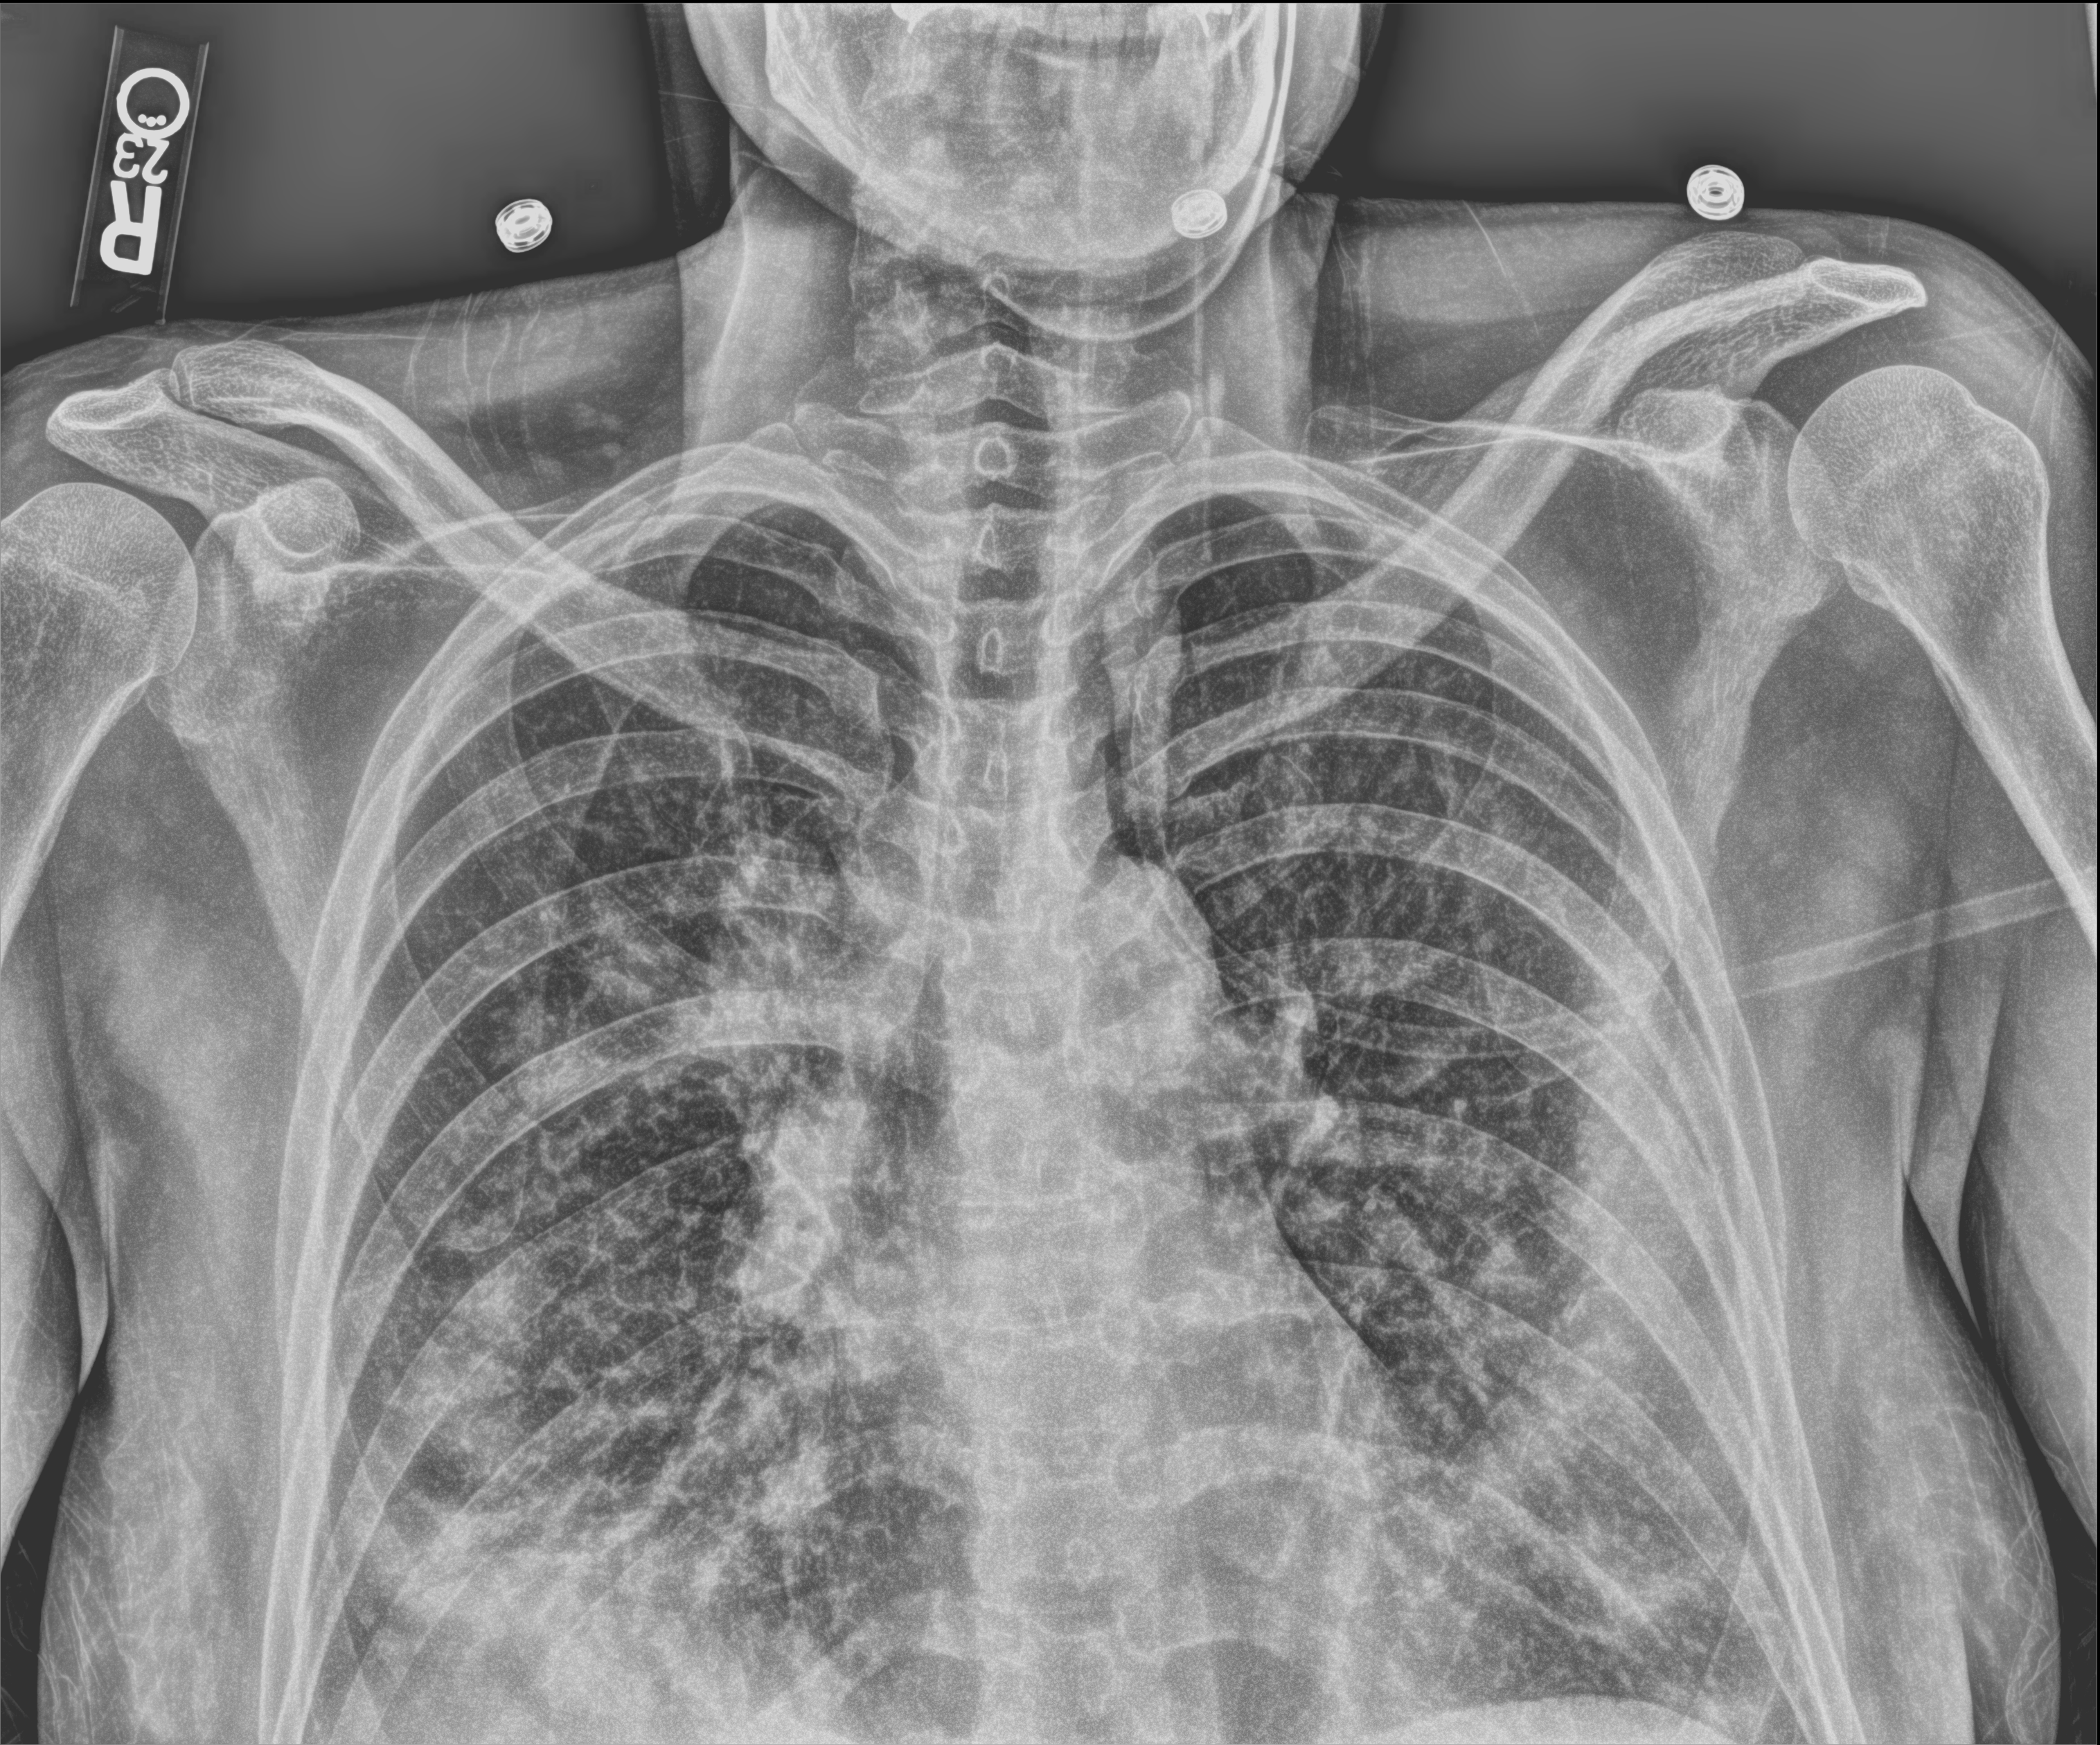
Bedside chest radiograph (computed radiography), anteroposterior (AP) projection. Patient hospitalised with COVID-19; female, aged 18–59 years.
Hospital-stay facts (about this admission, not read from this image; timing relative to this image not recorded): admitted to intensive care during this hospital stay: yes.